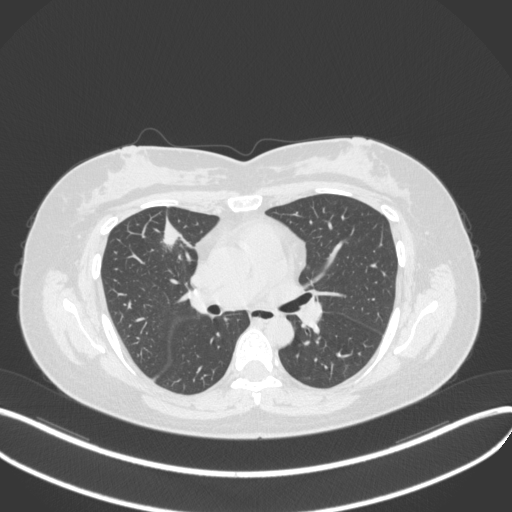
Chest CT, one axial slice. Position 181 of 272 along the scan axis. Reconstruction kernel B31f. 120 kVp. Lung window (W 1500 / L -600 HU). 1 mm slice thickness. 512 × 512 image matrix, field of view 400 × 400 mm. Female patient, age 42 years. From the clinical record (not read from this slice): clinical TNM (as recorded): T1b N0 M0.
Structures marked on this image (bounding box drawn by a radiologist):
- lung tumour (recorded histology: adenocarcinoma): bounding box (x1, y1, x2, y2) in pixels: (158, 215, 187, 254)